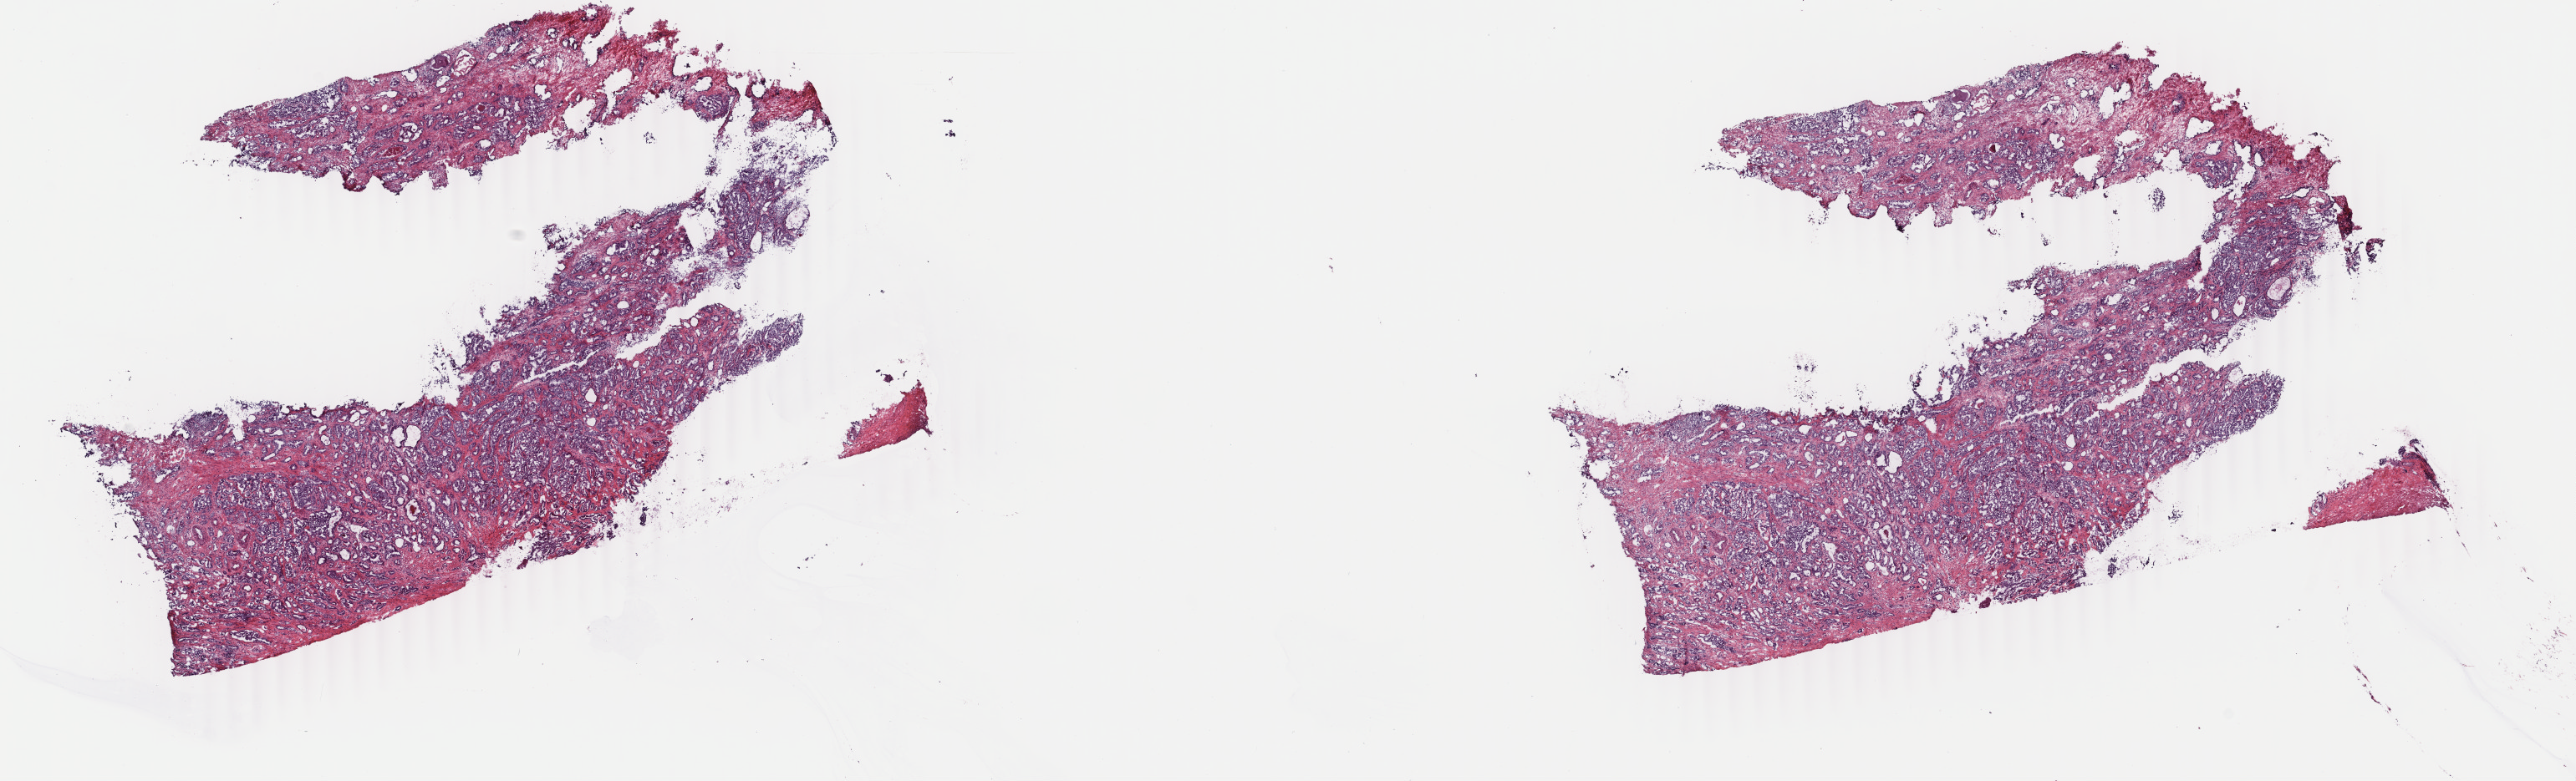
Whole-slide histology image, H&E, a low-resolution overview of the entire scanned area, about 24.5 x 7.4 mm (acquisition: 40x scan), frozen section from the top of the tissue portion, prostate, primary tumour sample. Male, age 61 years at initial diagnosis. Gleason score: 7 (3+4). Pathologist review of this section (percent, as recorded): tumour cells 70%, tumour nuclei 80%, normal cells 5%, stromal cells 25%, necrosis 0%. Infiltration values recorded for this section: lymphocyte infiltration 0%, monocyte infiltration 0%, neutrophil infiltration 0%.
- diagnosis: Adenocarcinoma, NOS